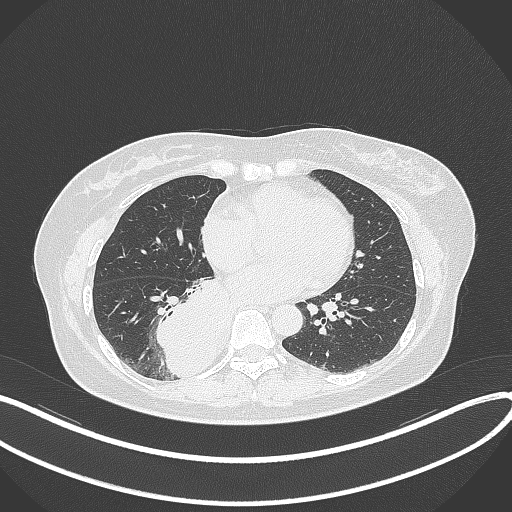
Chest CT, one axial slice. Position 146 of 331 along the scan axis. Reconstruction kernel B70f. 120 kVp. Lung window (W 1500 / L -600 HU). 1 mm slice thickness. 512 × 512 image matrix, field of view 400 × 400 mm. Female patient, age 54 years. From the clinical record (not read from this slice): clinical TNM (as recorded): T4 N0 M0.
Structures marked on this image (bounding box drawn by a radiologist):
- lung tumour (recorded histology: adenocarcinoma): box from (x=158, y=275) to (x=232, y=378) px